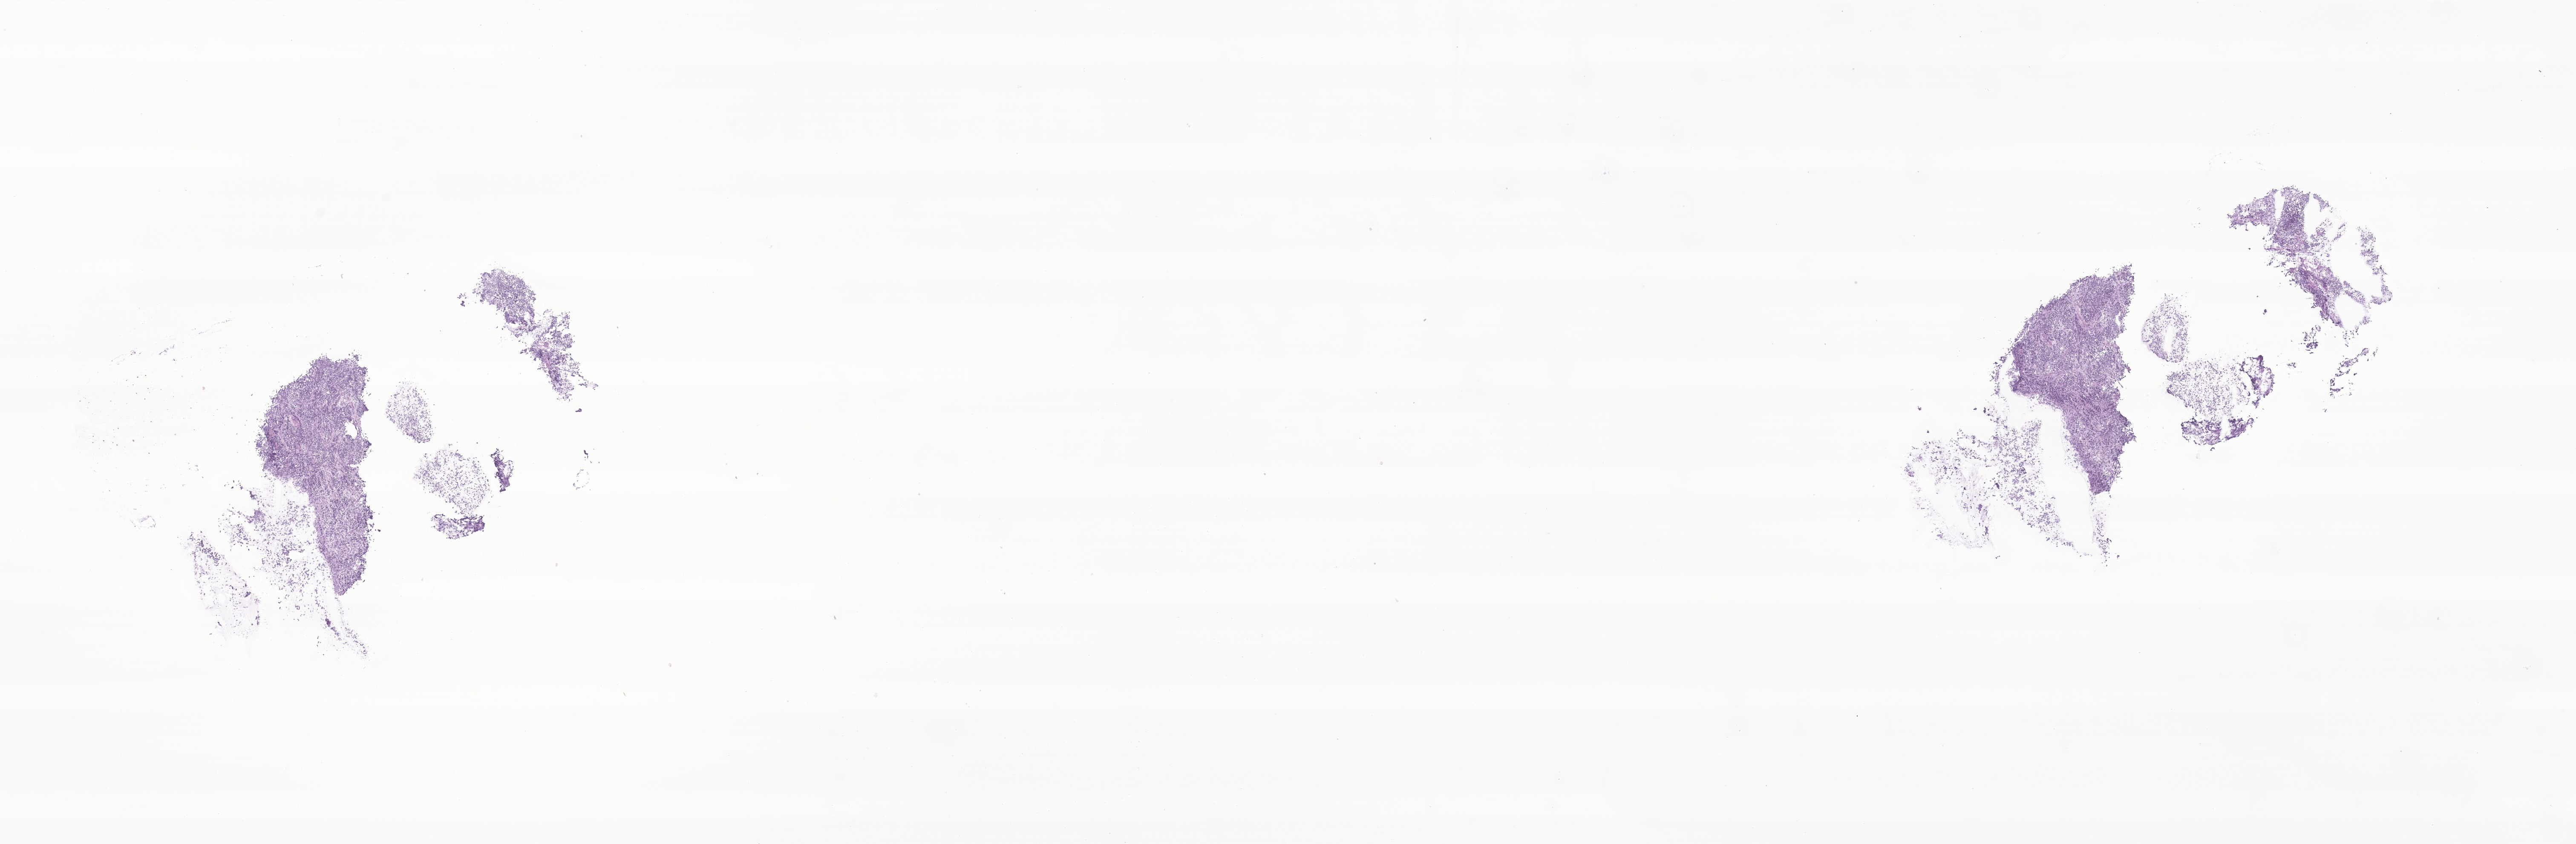
Haematoxylin and eosin whole-slide image of tumor tissue from the brain, shown as a low-resolution overview of the whole scanned area (about 25.5 x 8.4 mm); cryosection (OCT / tissue freezing medium). Patient: male, age 138 months.
Recorded diagnosis: Medulloblastoma, NOS.